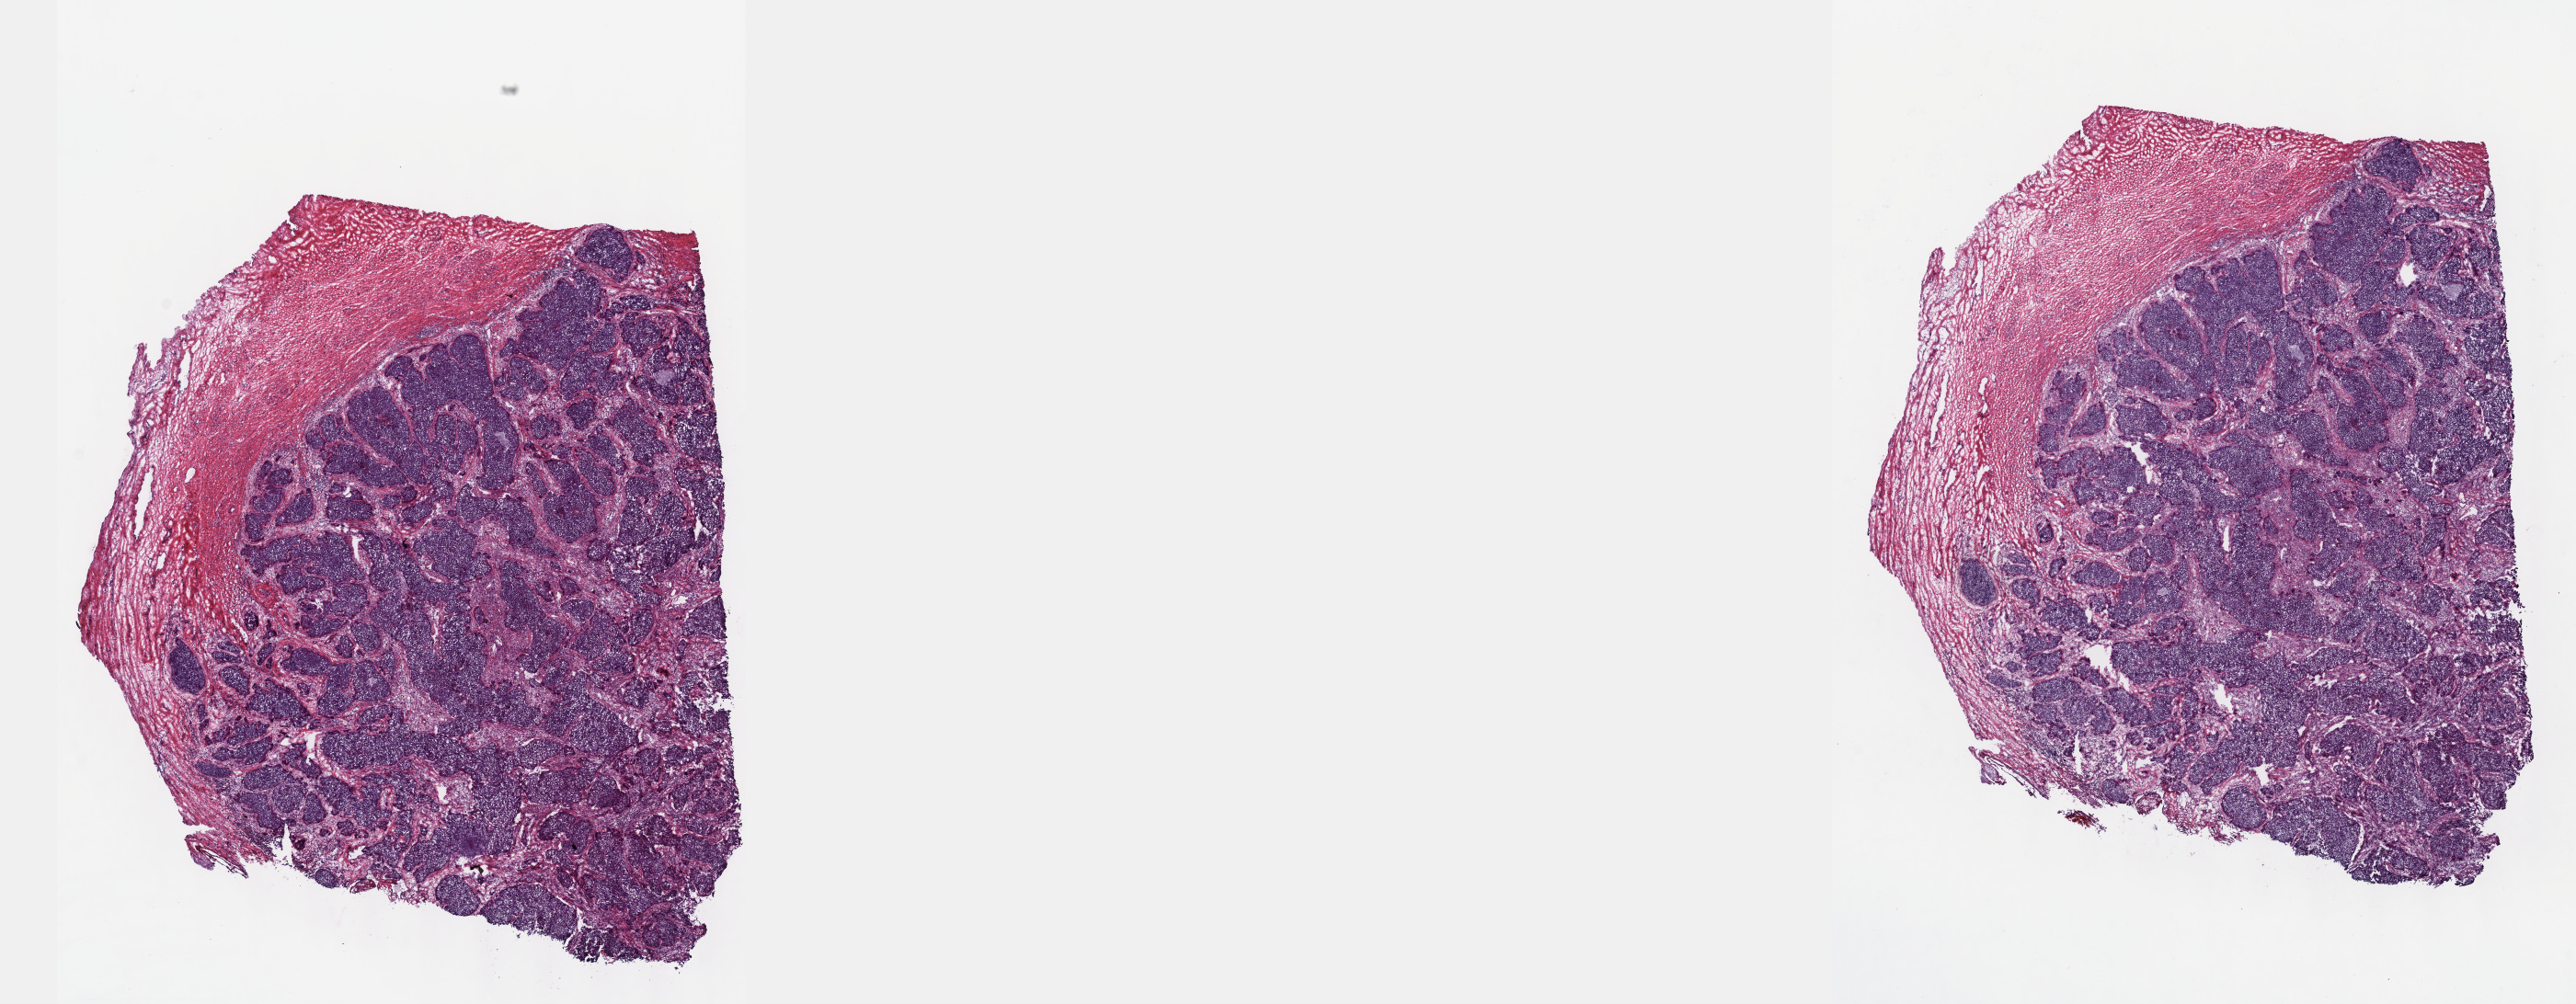
Whole-slide histology image, H&E-stained, whole scanned area (about 22.6 x 8.8 mm, from a 40x scan) shown as a low-resolution overview. Frozen section from the top of the tissue portion. Primary tumour sample from the cervix. Patient: female, age at initial diagnosis 64 years. Histologic grade: G2 (moderately differentiated). Slide review estimates, as recorded: tumour cells 80%, tumour nuclei 90%, normal cells 10%, stromal cells 10%, necrosis 0%. Inflammatory infiltration, as recorded: lymphocyte infiltration 0%, monocyte infiltration 0%, neutrophil infiltration 0%.
• diagnosis: Squamous cell carcinoma, large cell, nonkeratinizing, NOS (cervix uteri)
• FIGO stage: IB1